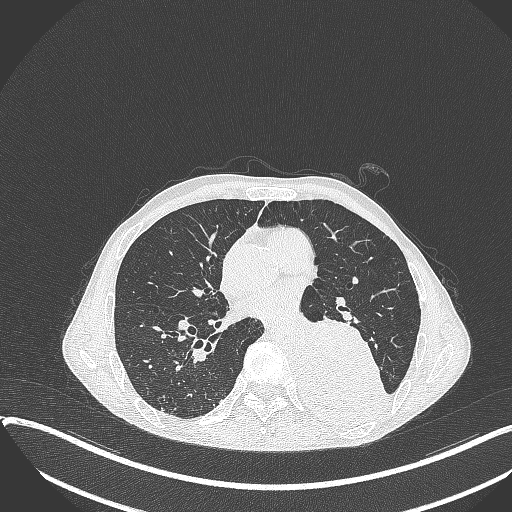
Chest CT, one axial slice. Position 176 of 401 along the scan axis. Lung window (W 1500 / L -600 HU). 512 × 512 image matrix, field of view 400 × 400 mm. Patient: male, 57 years. From the clinical record (not read from this slice): clinical TNM (as recorded): T4 N0 M0.
Outlined on this slice (rectangle marked by the reading radiologist):
- lung tumour (recorded histology: squamous cell carcinoma): bounding box <294,313,390,430> (left, top, right, bottom; pixels)